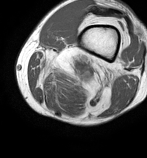
MRI of an extremity soft-tissue mass, one axial slice. Slice 18 of 86 in the series (ordered by position). MR volume resampled by the dataset authors to the PET/CT grid (not the native acquisition matrix). 3.27 mm slice thickness. 147 × 158 image matrix, field of view 144 × 154 mm. Male patient. From the clinical record (not read from this slice): histological type: undifferentiated pleomorphic liposarcoma; grade: high; site of the primary tumour: left thigh.
Annotated regions visible in this slice (expert contour drawn on MRI and transferred to this co-registered scan by the dataset authors):
- gross tumour volume including surrounding oedema: bounding box [x1, y1, x2, y2] px = [37, 51, 115, 91]